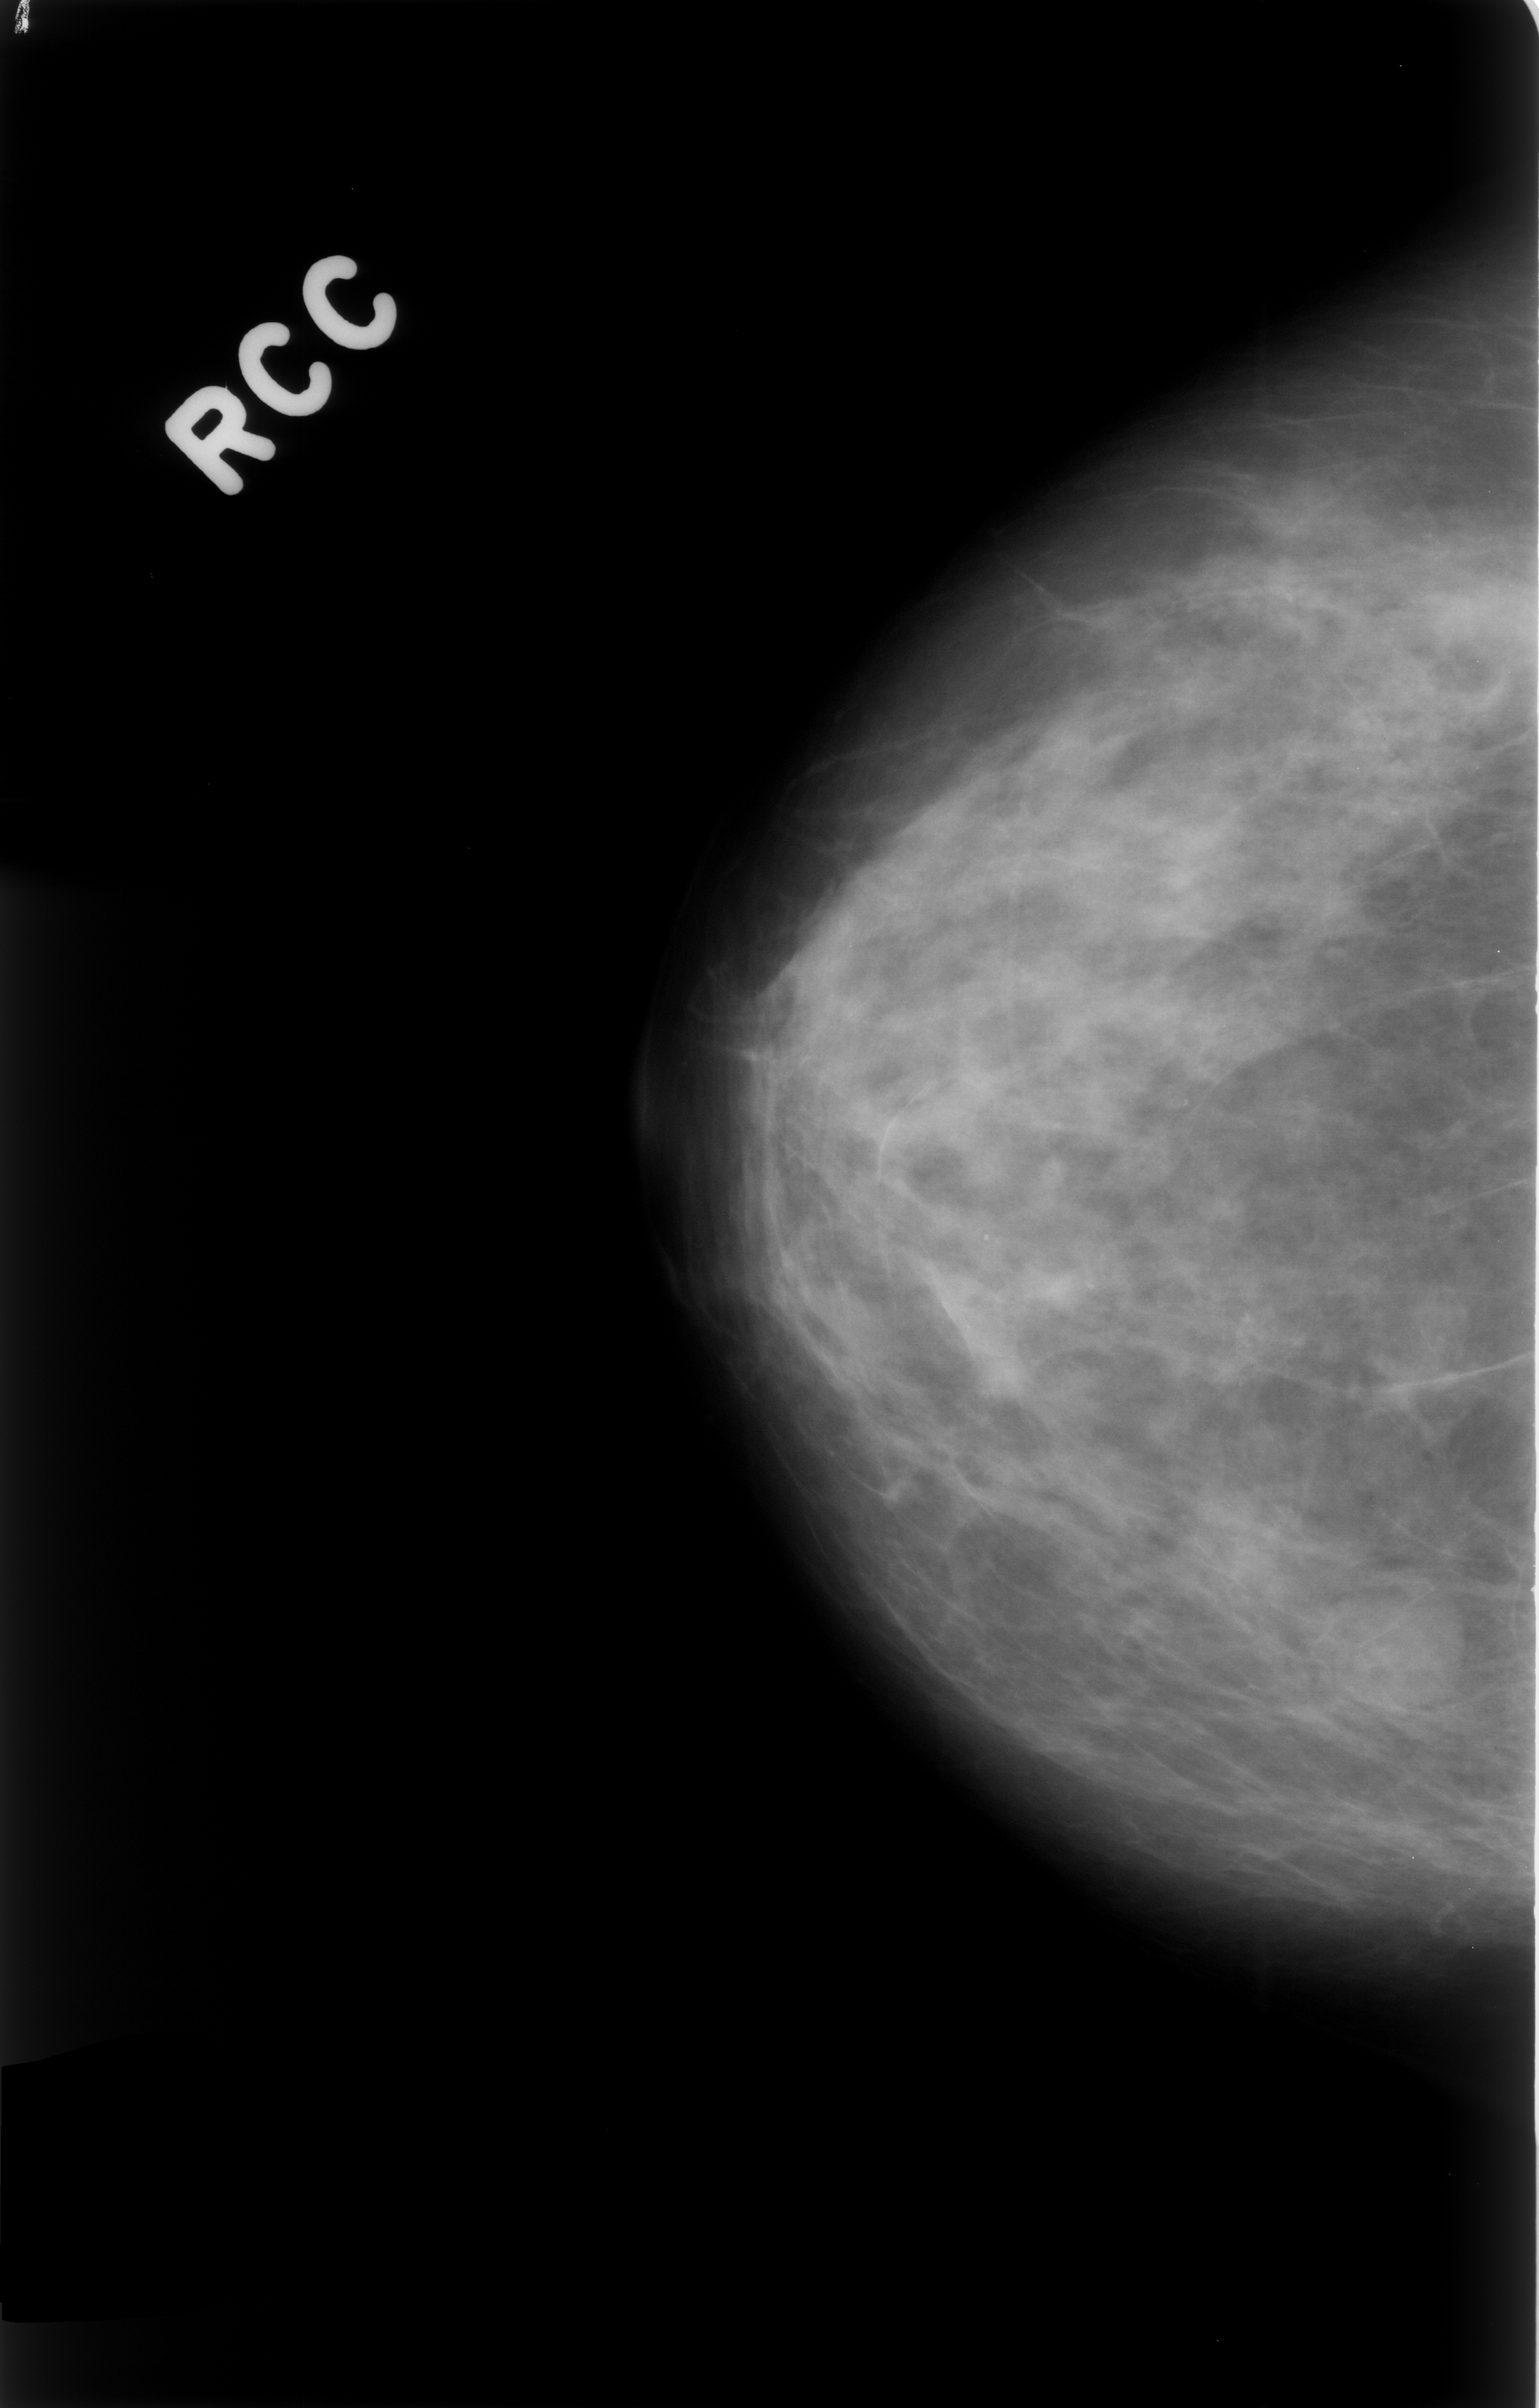
Digitized screen-film mammogram, right breast, craniocaudal (CC) view.
- Abnormality record for this image: mass, shape round, margins circumscribed; BI-RADS assessment category 4; subtlety rating 5 on a 1 (subtle) to 5 (obvious) scale; pathology result (as recorded, not read from the image): benign.